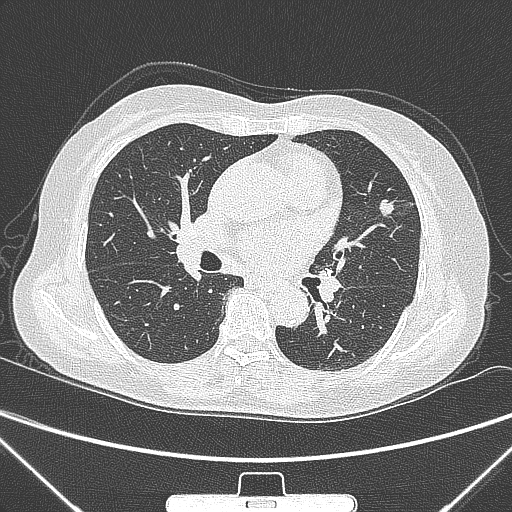
Chest CT, one axial slice; position 148 of 300 along the scan axis; lung window (W 1500 / L -600 HU); 1 mm slice thickness; 512 × 512 image matrix, field of view 350 × 350 mm. Female patient, age 70 years. From the clinical record (not read from this slice): clinical TNM (as recorded): T1b N0 M0; histopathological grade: G2.
Annotated regions visible in this slice (rectangle marked by the reading radiologist):
- lung tumour (recorded histology: adenocarcinoma): bounding box (x1, y1, x2, y2) in pixels: (375, 192, 409, 233)